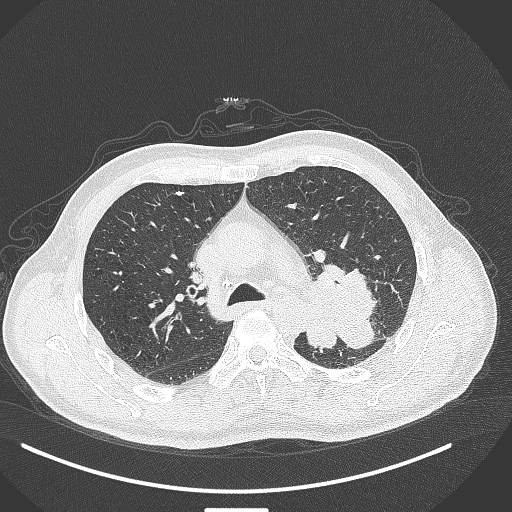
Chest CT, one axial slice; slice 282 of 429 in the series (ordered by position); 120 kVp; lung window (W 1500 / L -600 HU); 1 mm slice thickness; 512 × 512 image matrix, field of view 400 × 400 mm. Patient: male, 55 years. From the clinical record (not read from this slice): clinical TNM (as recorded): T3 N0 M1c.
Annotated regions visible in this slice (bounding box drawn by a radiologist):
- lung tumour (recorded histology: adenocarcinoma): bounding box <301,258,383,354> (left, top, right, bottom; pixels)